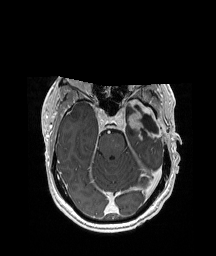
Brain MRI from a brain-tumour surgery series, one axial slice. T1-weighted post-contrast. 1 mm slice thickness. 216 × 256 image matrix. From the clinical record (not read from this slice): histopathology: Glioblastoma; WHO grade: 4; IDH mutation: no; tumour location: Left Anterior/Superior Temporal.
Annotated regions visible in this slice (outlined manually by an expert reader):
- previous resection cavity: bounding box (x1, y1, x2, y2) in pixels: (134, 105, 158, 134)
- tumour: (133, 99, 158, 144)